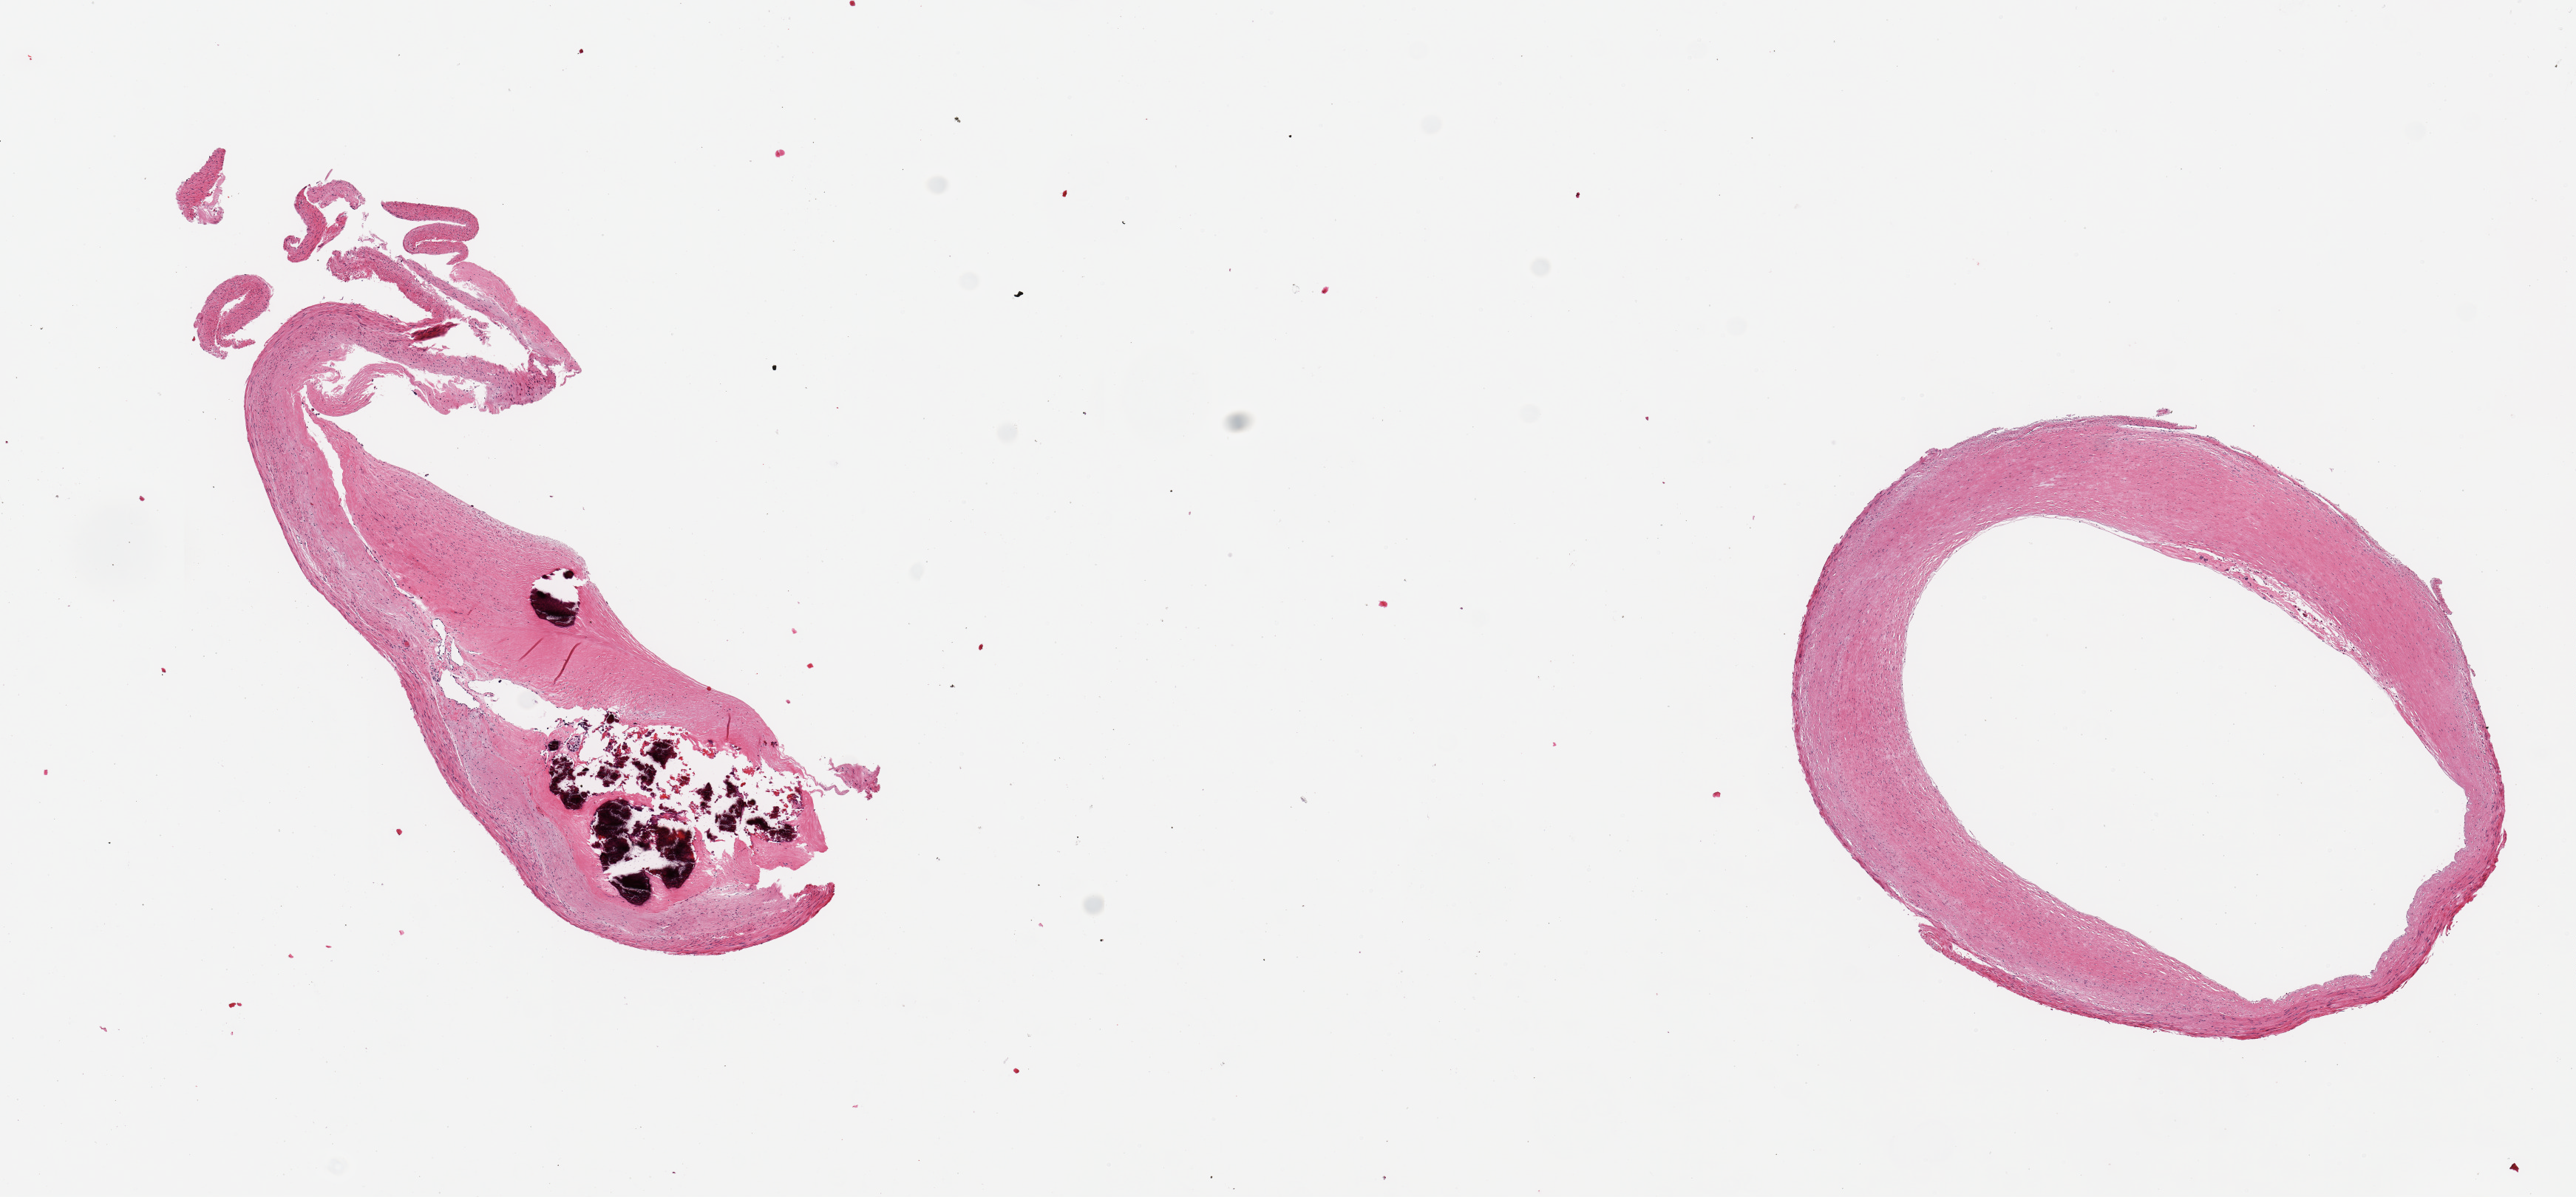
Whole-slide image, hematoxylin and eosin (H&E) stain, shown as a low-resolution overview of the whole scanned area (about 13.8 x 6.4 mm, from a 20x scan). PAXgene-fixed paraffin-embedded (PFPE) section. Section of coronary artery (target tissue). Donor tissue sample. Male donor.
Review note (as recorded): 2 pieces, ~50% occlusive calcifying atherosis.